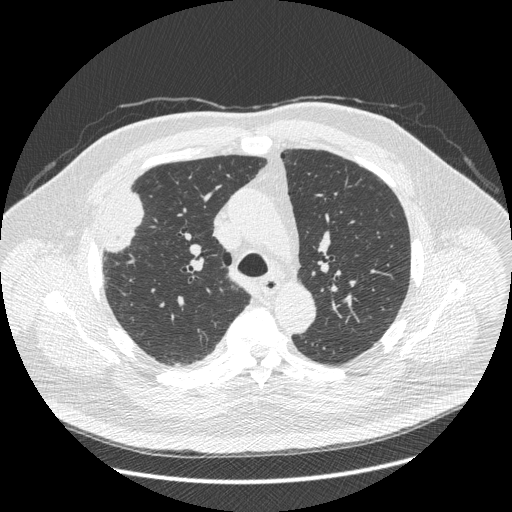
Low-dose screening chest CT, one axial slice. Position 295 of 426 along the scan axis. Reconstruction kernel STANDARD. Lung window (W 1500 / L -600 HU). 1.25 mm slice thickness. 512 × 512 image matrix, field of view 400 × 400 mm.
Outlined on this slice (expert manual segmentation):
- lesion 1 (tumor, upper lobe of right lung): bounding box <106,192,143,252> (left, top, right, bottom; pixels)